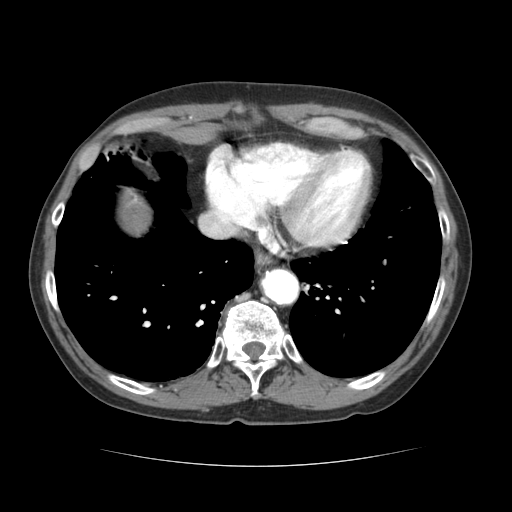
Contrast-enhanced abdominal CT (liver protocol), one axial slice. Slice 62 of 69 in the series (ordered by position). Reconstruction kernel STANDARD. 120 kVp. Soft-tissue window (W 400 / L 40 HU). 512 × 512 image matrix. Case-level facts recorded for this patient, not image findings: diagnosis: hepatocellular carcinoma (patient treated with transarterial chemoembolisation; whether this scan precedes or follows treatment is not stated here); TNM stage (as recorded): Stage-II; Child-Pugh class: B; tumour differentiation: poorly differentiated; tumour nodularity: multinodular.
Annotated regions visible in this slice (semi-automatic segmentation, software-assisted and operator-edited):
- liver parenchyma outside the tumour (the mass and vessels are separate outlines, so this box may not span the whole liver): box from (x=122, y=197) to (x=150, y=232) px